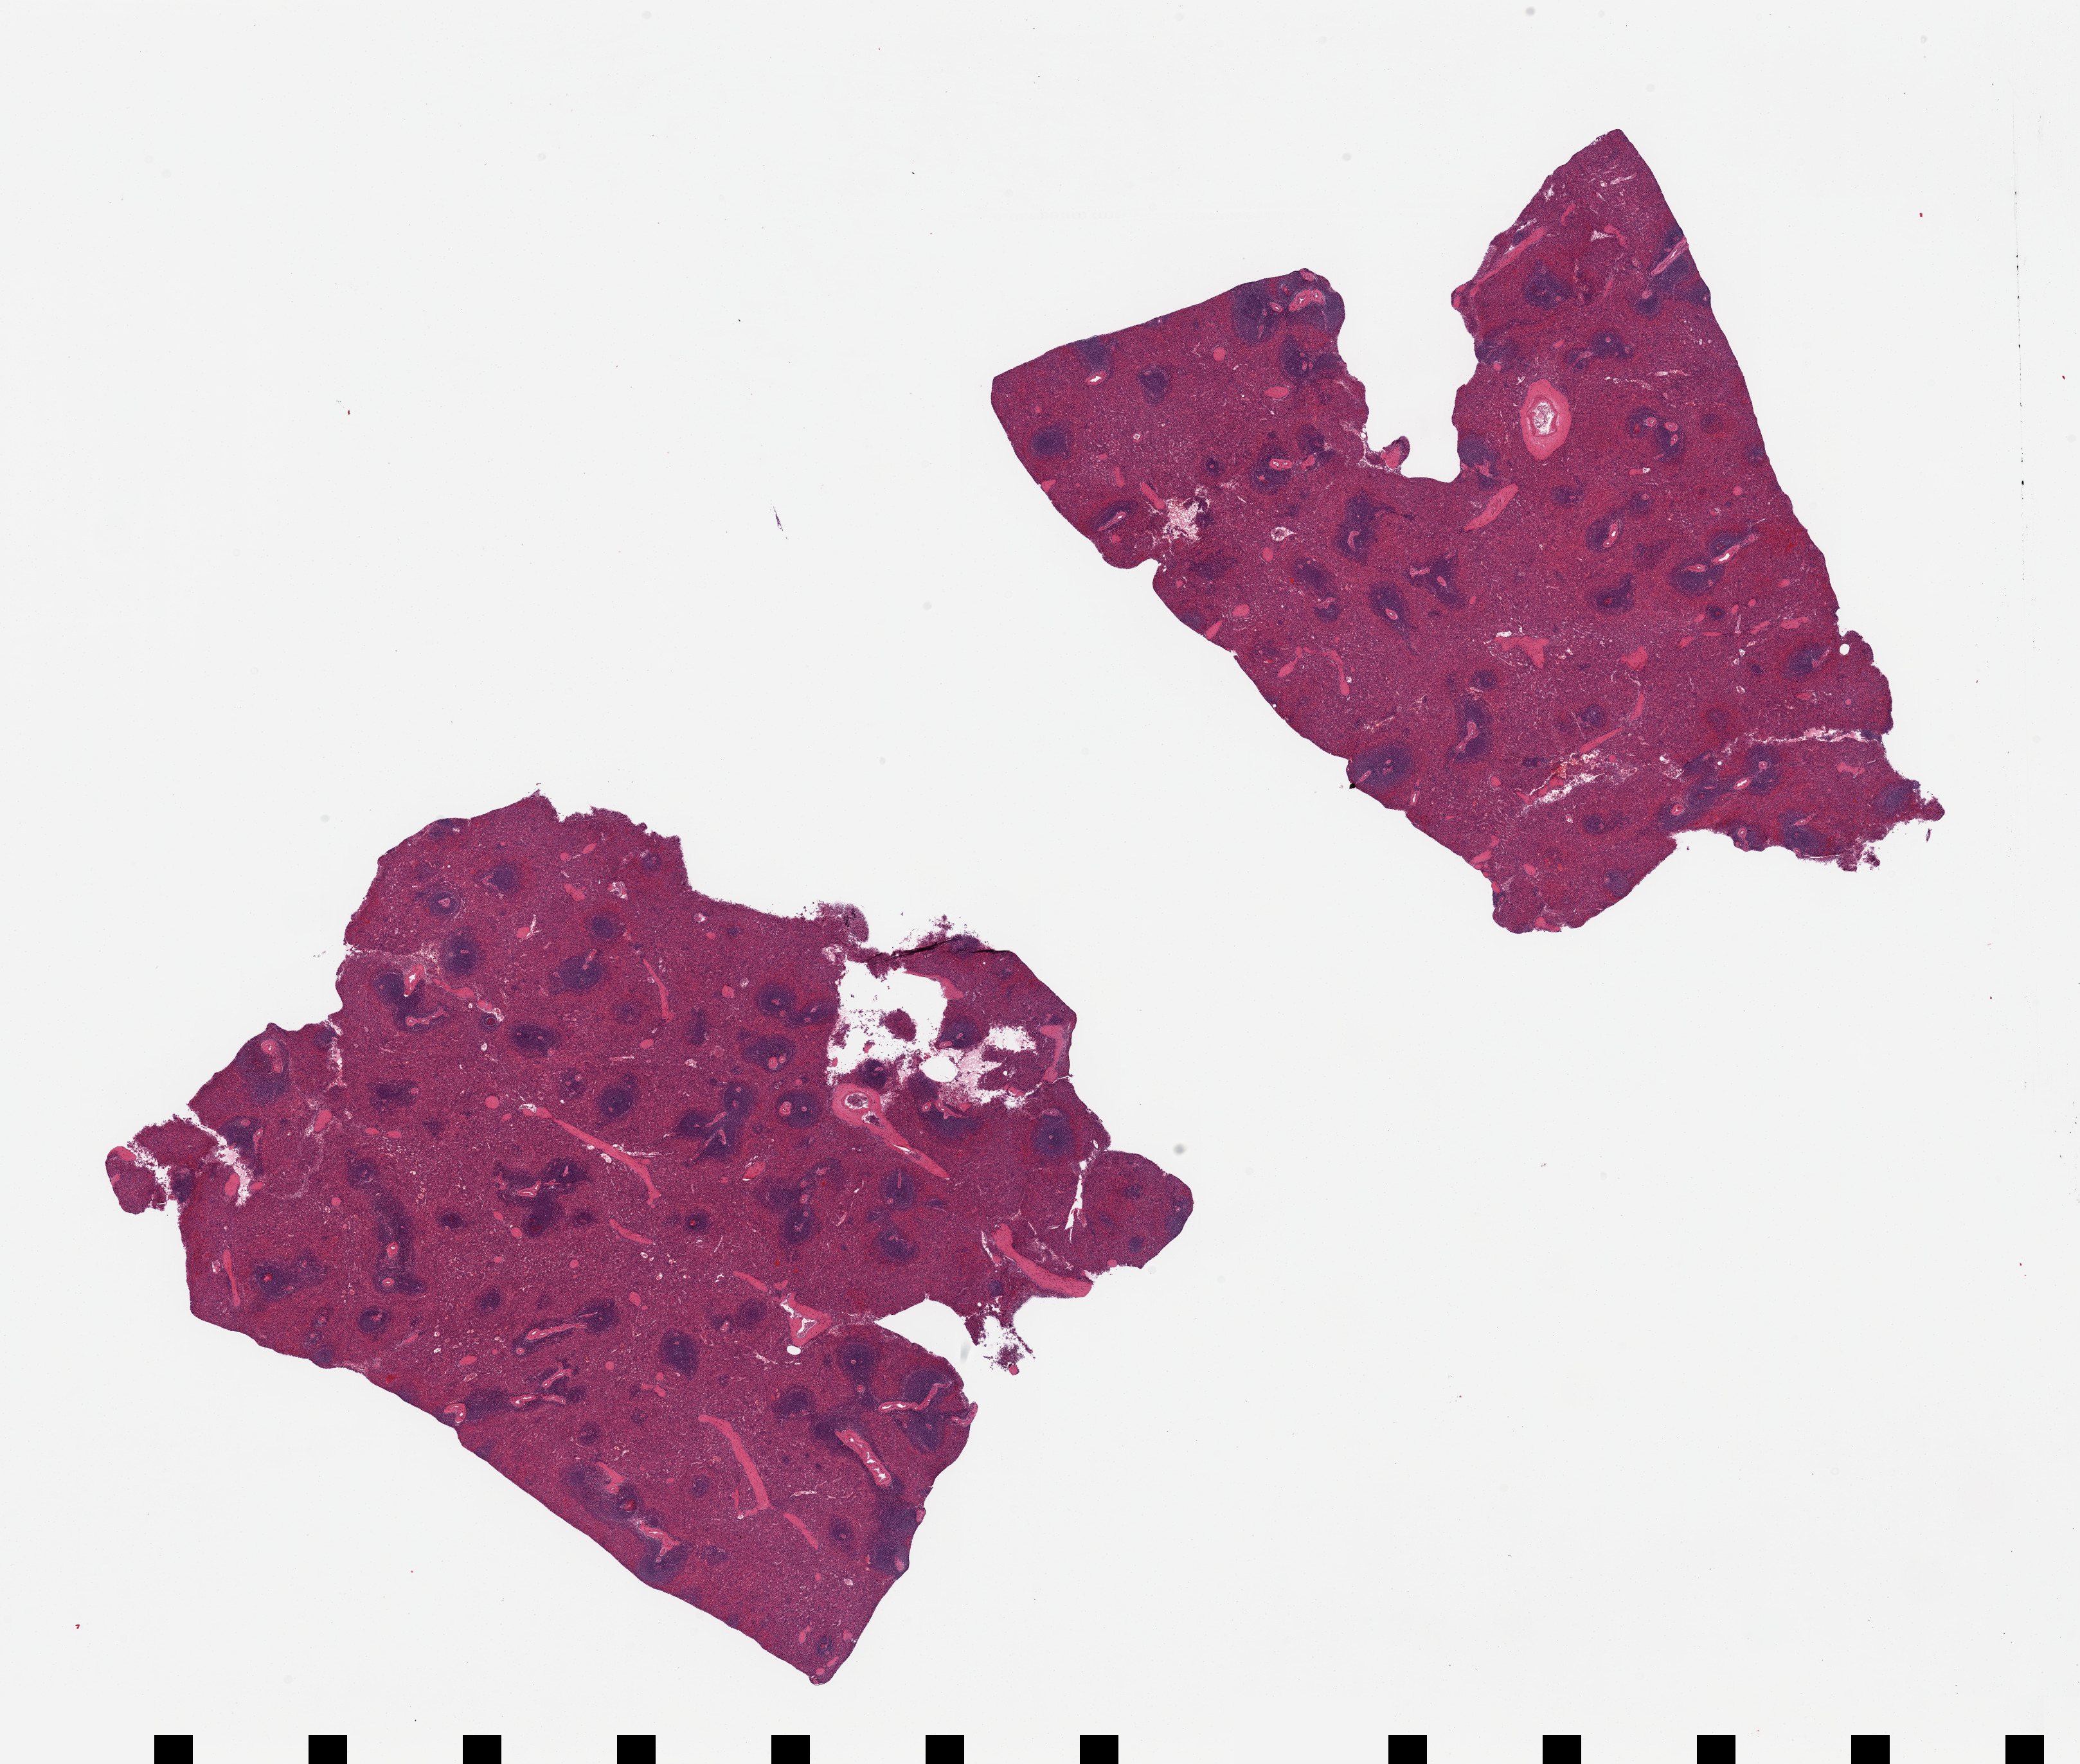
Whole-slide image, hematoxylin and eosin (H&E) stain, brightfield, a low-resolution overview of the entire scanned area, about 25.6 x 21.7 mm. PAXgene-fixed, paraffin-embedded tissue. Sampled site (target tissue): spleen. Tissue donor sample. Female donor.
* review note (as recorded): 2 pieces, mild congestion